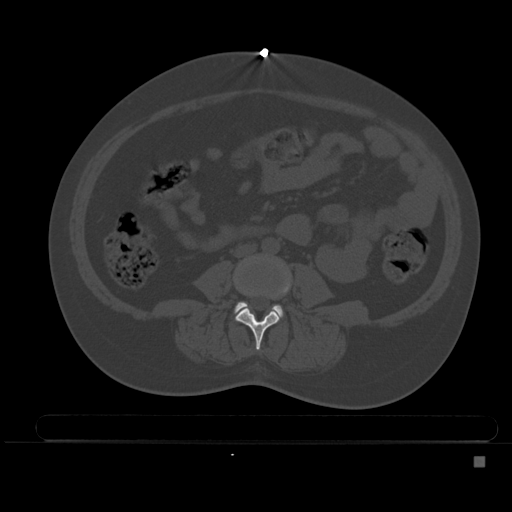
CT including the spine, one axial slice. Position 142 of 495 along the scan axis. Bone window (W 1800 / L 400 HU). 1.5 mm slice thickness. 512 × 512 image matrix. Patient: female, 33 years. Case-level facts recorded for this patient, not image findings: primary cancer: breast; vertebrae with lytic lesions (as recorded): T1.
Outlined on this slice (semi-automatically segmented with operator editing):
- L3 vertebra: box from (x=235, y=268) to (x=291, y=350) px
- L4 vertebra: (x=235, y=302)–(x=283, y=316)